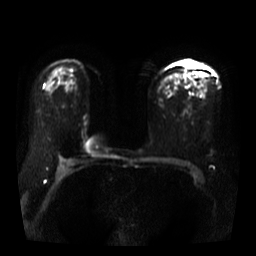
Breast MRI, one axial slice. Position 24 of 40 along the scan axis. Diffusion-weighted series; image 2 of 4 stored at this slice position (different b-values; order by instance number). 3 T. 5 mm slice thickness. 256 × 256 image matrix, field of view 360 × 360 mm. Female patient.
Outlined on this slice (expert manual segmentation):
- tumour on diffusion-weighted imaging: bounding box <185,62,195,67> (left, top, right, bottom; pixels)